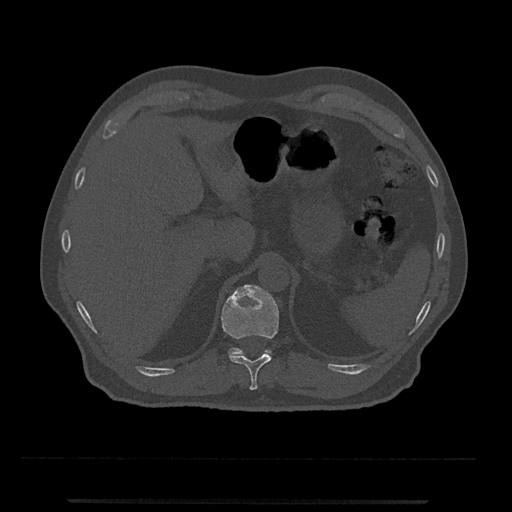
CT including the spine, one axial slice; position 448 of 797 along the scan axis; reconstruction kernel Br40s/3; 120 kVp; bone window (W 1800 / L 400 HU); 0.5 mm slice thickness; 512 × 512 image matrix. Patient: male, 63 years. From the clinical record (not read from this slice): primary cancer: prostate.
Structures marked on this image (semi-automatic segmentation, software-assisted and operator-edited):
- T11 vertebra: bounding box (x1, y1, x2, y2) in pixels: (221, 285, 279, 390)
- T12 vertebra: (229, 348, 272, 356)